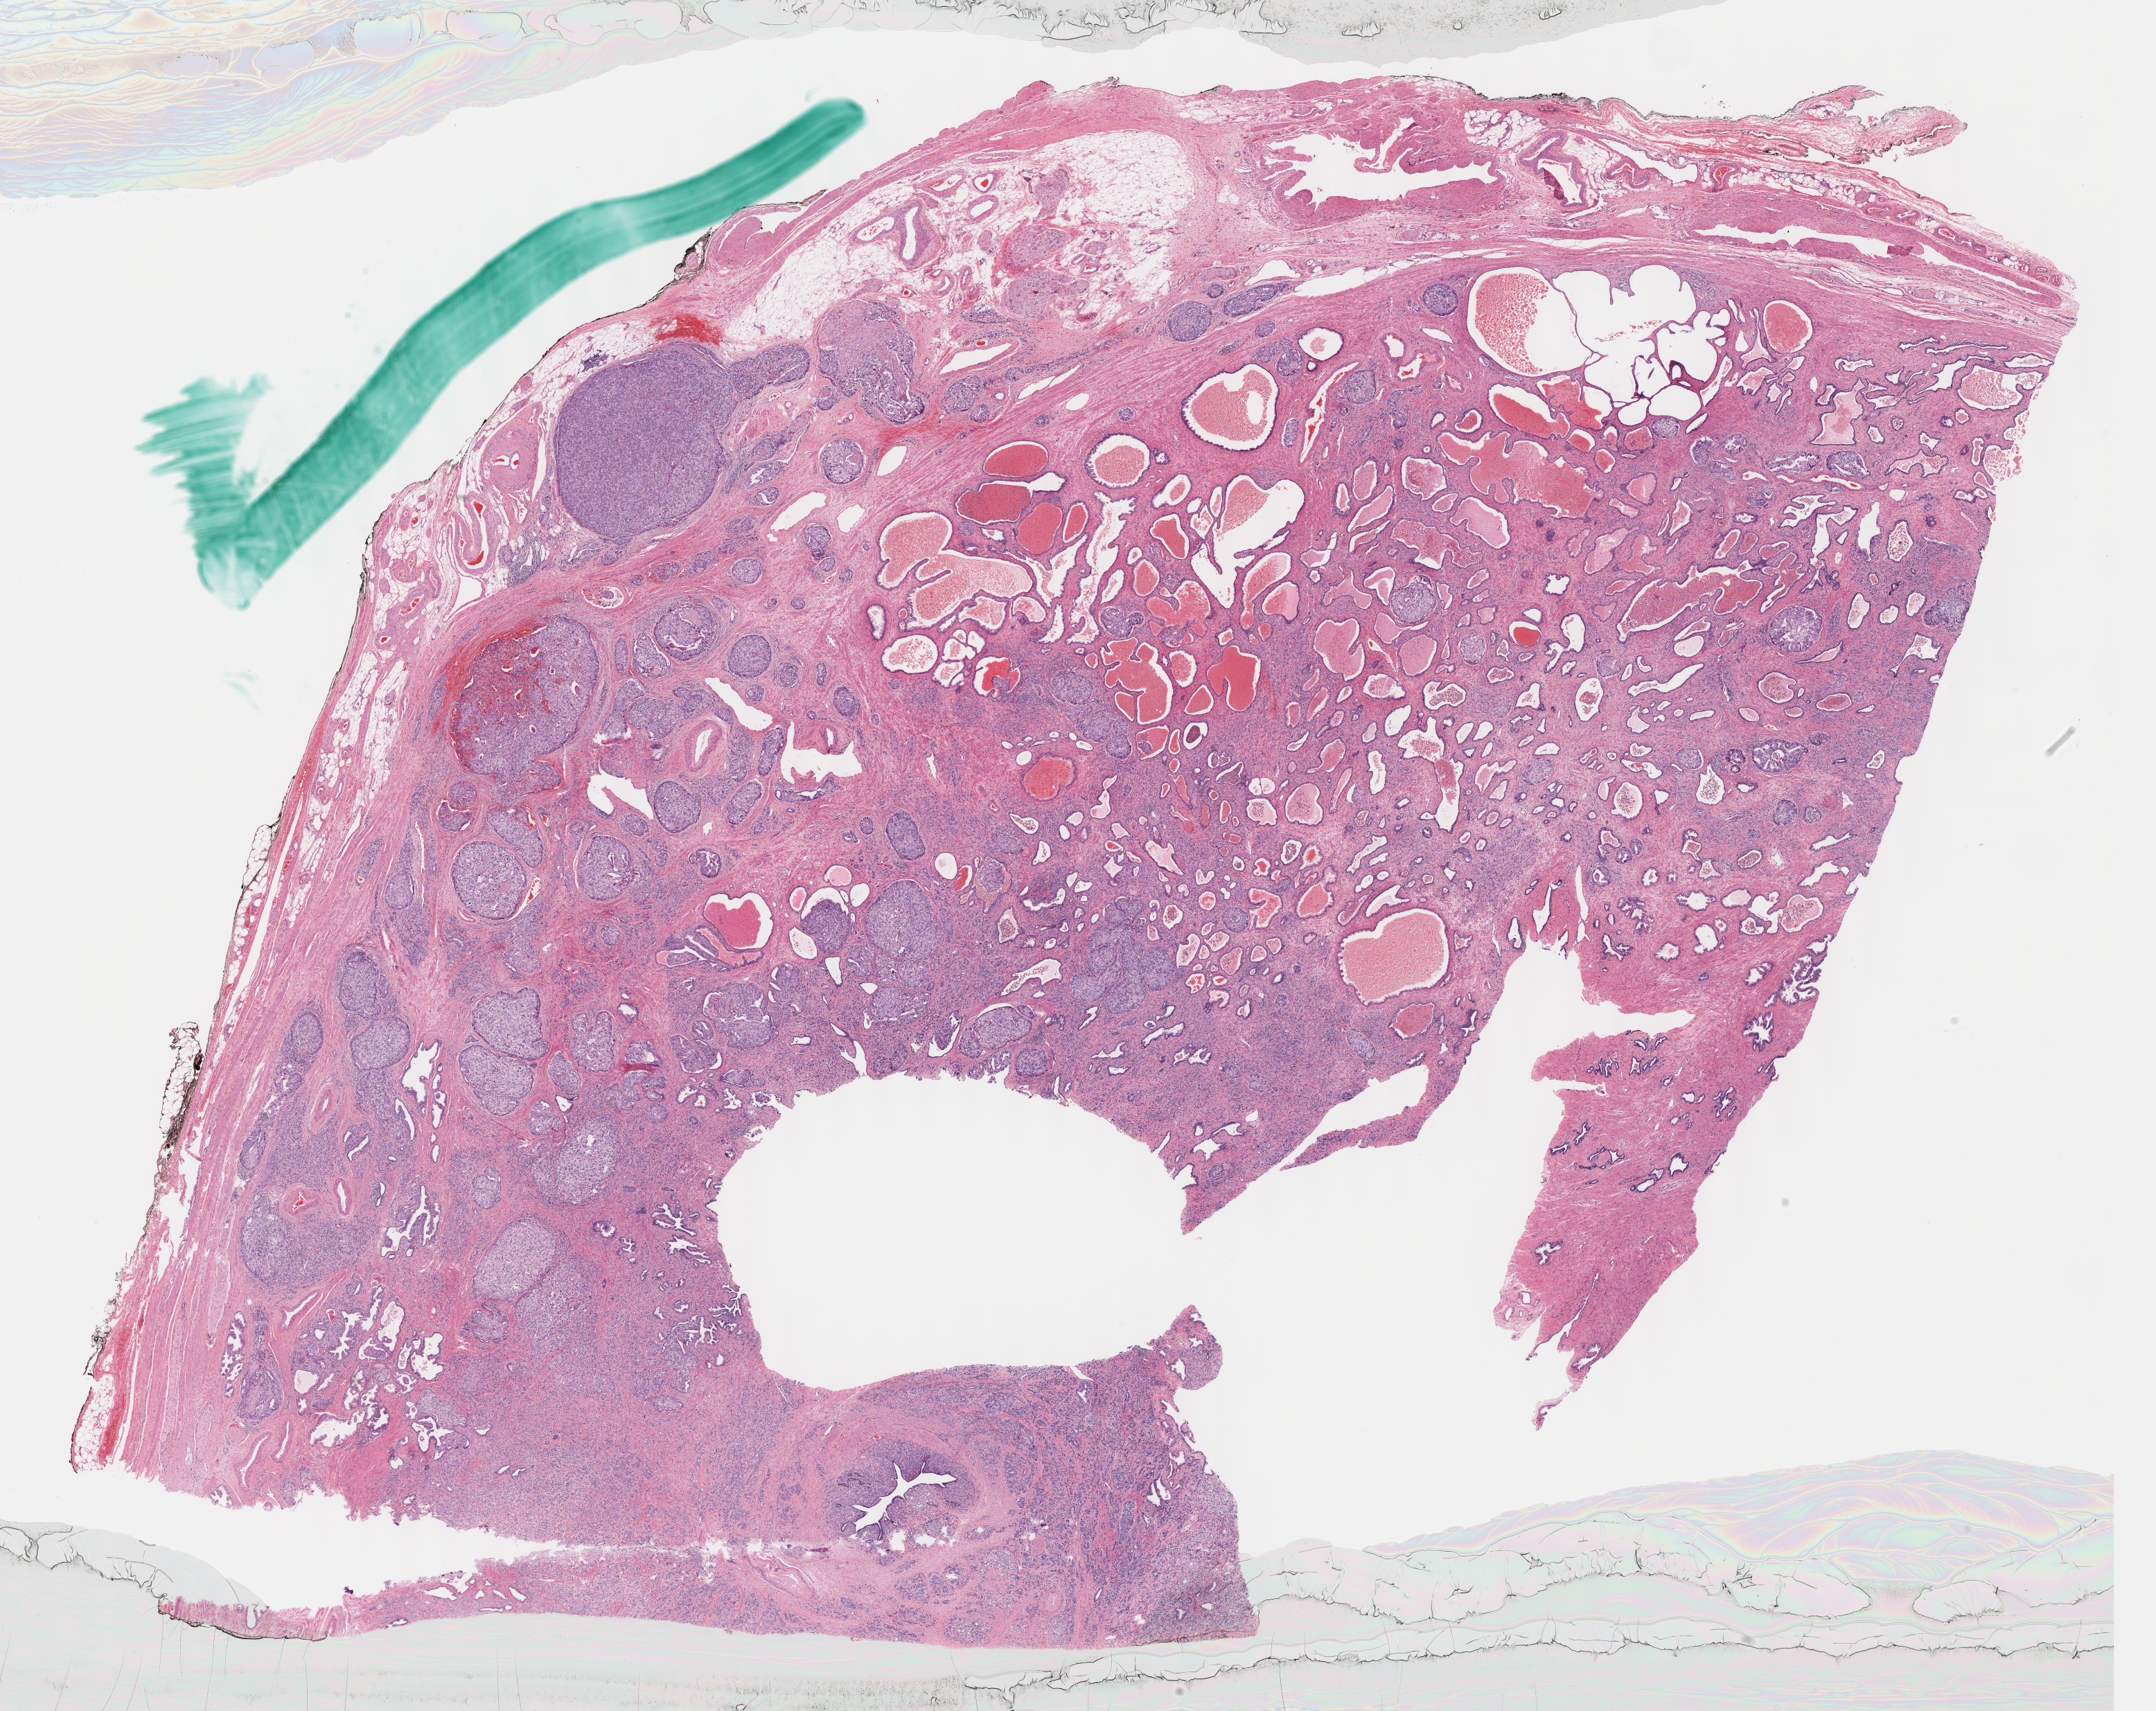
Whole-slide histology image, Hematoxylin and eosin (H&E) stained, low-resolution overview of the scanned area, about 25.1 x 20.0 mm. Formalin-fixed paraffin-embedded (FFPE) diagnostic section. Prostate, primary tumour sample. Male patient; age at initial diagnosis 64 years. Gleason score: 9 (5+4).
Diagnosis: Adenocarcinoma, NOS. Laterality: bilateral.